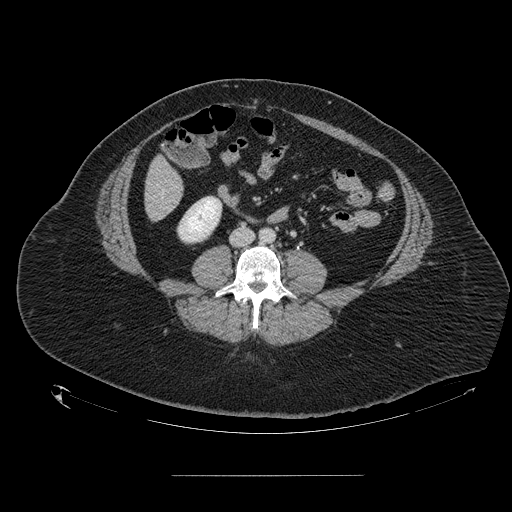
Contrast-enhanced abdominal CT, one axial slice. Position 21 of 164 along the scan axis. Intravenous contrast given. Soft-tissue window (W 400 / L 40 HU). 512 × 512 image matrix. Female patient, age 52 years. Case-level facts recorded for this patient, not image findings: diagnosis: colorectal cancer liver metastases, imaged before liver resection; multiple liver metastases: yes; largest metastasis: 3.5 cm; chemotherapy before resection: no.
Annotated regions visible in this slice (outlined manually by an expert reader):
- liver: bounding box [x1, y1, x2, y2] px = [146, 158, 183, 220]